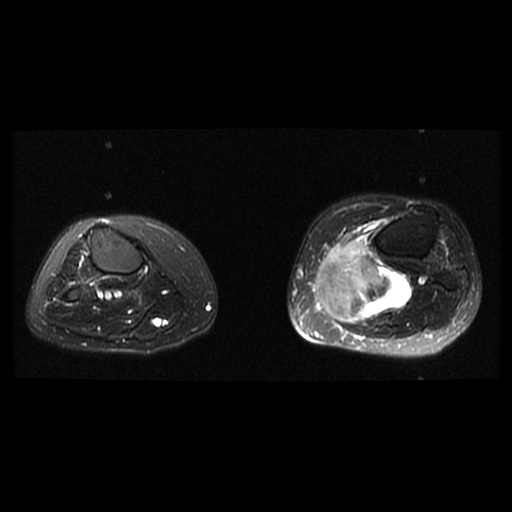
MRI of an extremity soft-tissue mass, one axial slice; position 21 of 38 along the scan axis; T2-weighted fat-saturated; 6 mm slice thickness; 512 × 512 image matrix. Female patient. From the clinical record (not read from this slice): histological type: extraskeletal high grade osteogenic sarcoma; grade: high; site of the primary tumour: left calf.
Outlined on this slice (outlined manually by an expert reader):
- gross tumour volume (mass): bounding box (x1, y1, x2, y2) in pixels: (316, 238, 414, 323)